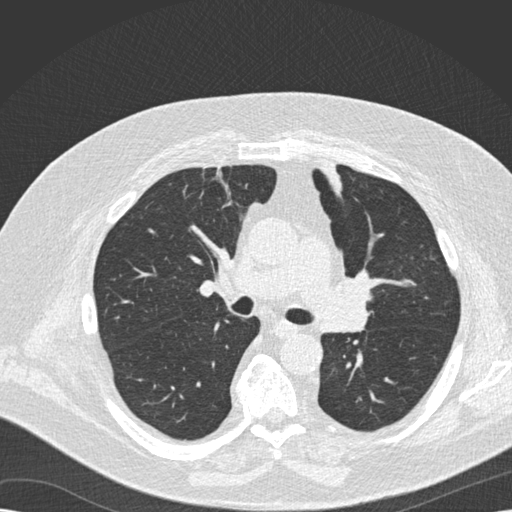
Low-dose screening chest CT, one axial slice. Slice 103 of 173 in the series (ordered by position). 120 kVp. Lung window (W 1500 / L -600 HU). 2 mm slice thickness. 512 × 512 image matrix, field of view 370 × 370 mm.
Outlined on this slice (manually delineated by an expert):
- lesion 1 (tumor, upper lobe of left lung): box from (x=319, y=161) to (x=346, y=194) px